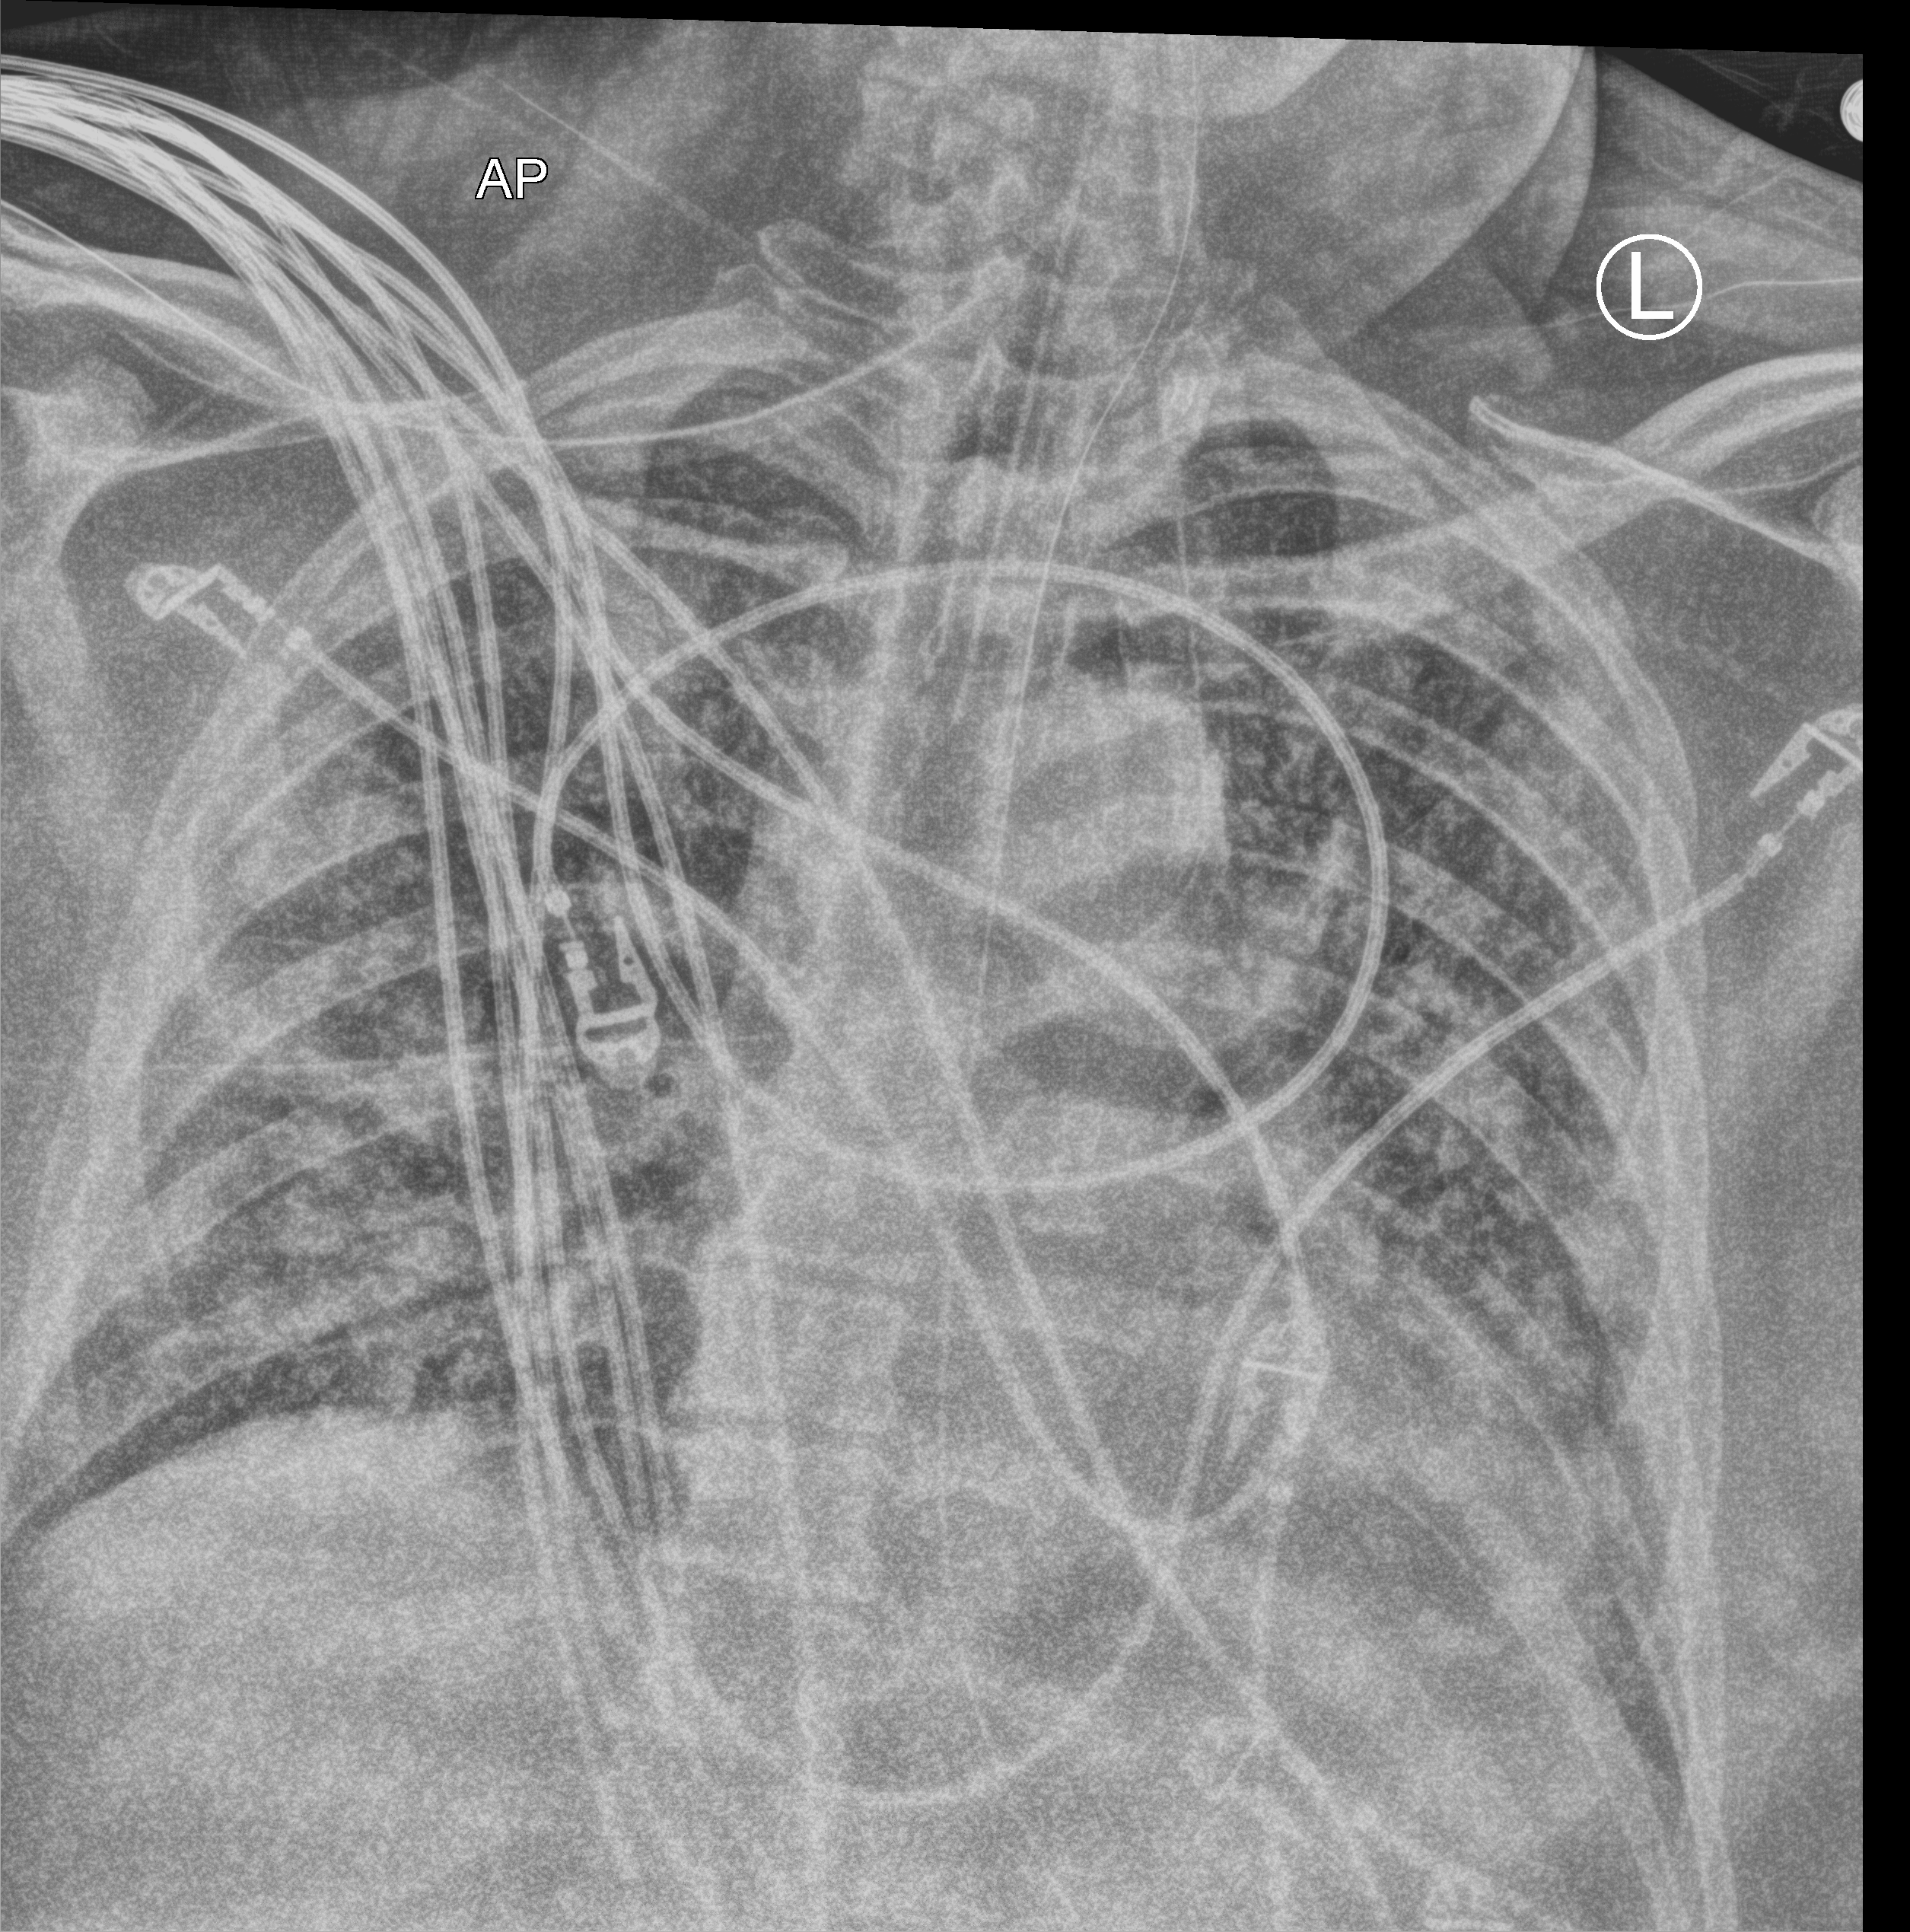
Chest X-ray (portable); anteroposterior (AP) projection. Patient hospitalised with COVID-19; male, aged 60–74 years.
From the hospital-stay record, not from the radiograph (when in the stay this image was taken is not recorded):
- chronic kidney disease (admission record): no